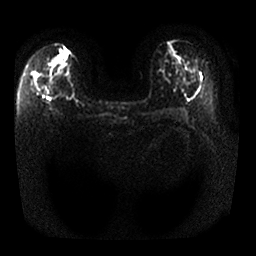
Breast MRI, one axial slice. Diffusion-weighted series; image 2 of 4 stored at this slice position (different b-values; order by instance number). 1.5 T. 4 mm slice thickness. 256 × 256 image matrix, field of view 340 × 340 mm. Female patient.
Outlined on this slice (expert manual segmentation):
- tumour on diffusion-weighted imaging: box from (x=37, y=77) to (x=49, y=88) px